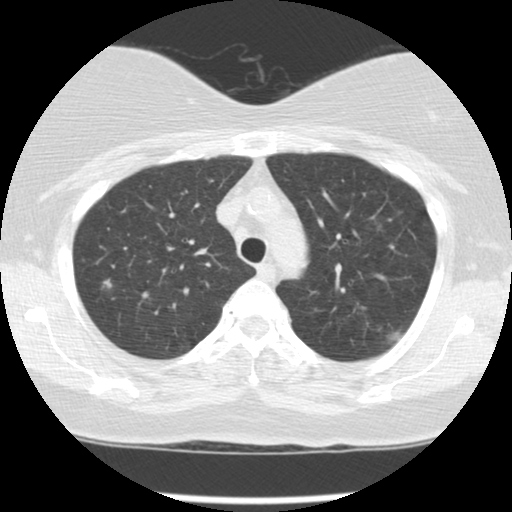
Low-dose screening chest CT, one axial slice. Position 101 of 127 along the scan axis. Reconstruction kernel STANDARD. 120 kVp. Lung window (W 1500 / L -600 HU). 2.5 mm slice thickness. 512 × 512 image matrix.
Outlined on this slice (expert manual segmentation):
- lesion 1 (tumor, upper lobe of left lung): bounding box <386,326,404,342> (left, top, right, bottom; pixels)